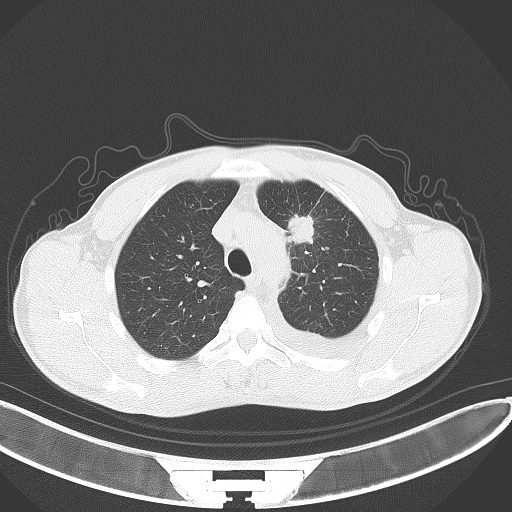
Chest CT, one axial slice. Position 101 of 130 along the scan axis. Reconstruction kernel B70f. Lung window (W 1500 / L -600 HU). 512 × 512 image matrix, field of view 400 × 400 mm. Male patient, age 49 years. Case-level facts recorded for this patient, not image findings: clinical TNM (as recorded): T1c N1 M1.
Outlined on this slice (rectangle marked by the reading radiologist):
- lung tumour (recorded histology: adenocarcinoma): bounding box (x1, y1, x2, y2) in pixels: (283, 210, 318, 246)